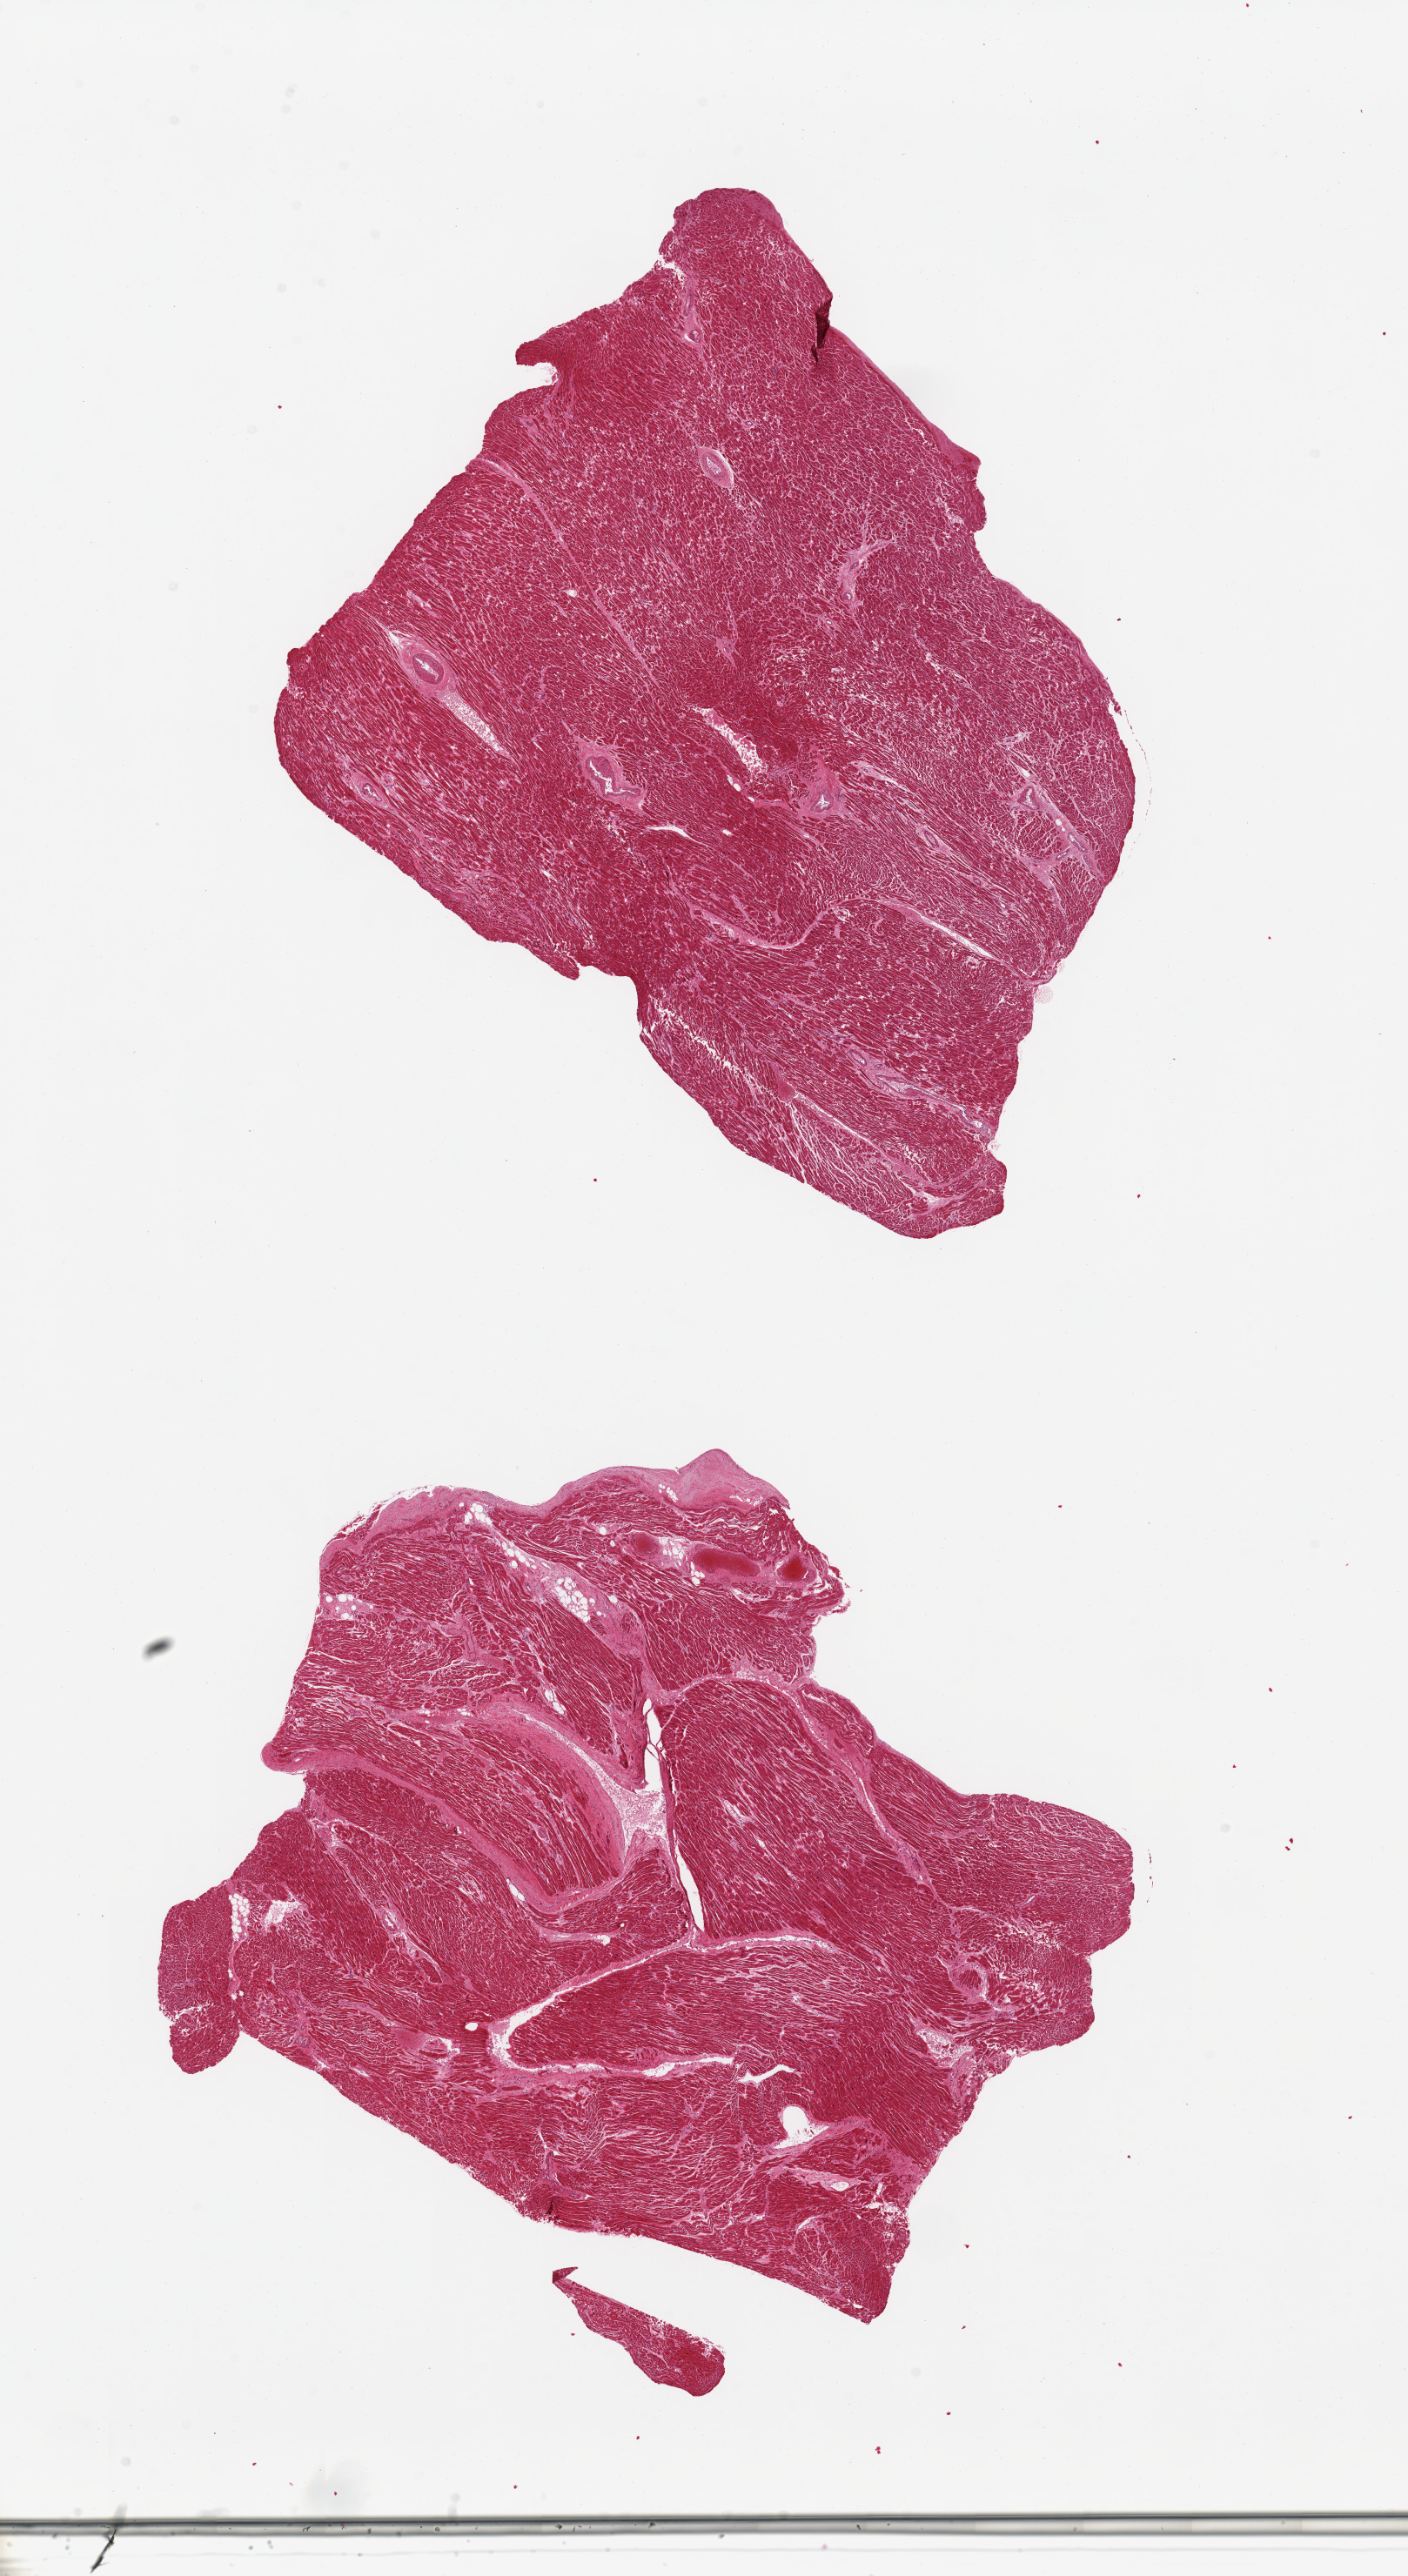
Whole-slide image, haematoxylin and eosin stain, shown as a low-resolution overview of the whole scanned area (about 12.8 x 23.4 mm, acquisition: 20x scan), PAXgene-fixed, paraffin-embedded tissue, sampled site (target tissue): heart, tissue donor sample. Male donor.
• pathologist's review note for this sample: 2 pieces; interstitial fibrosis, patchy eosinophilia (?ischemia)